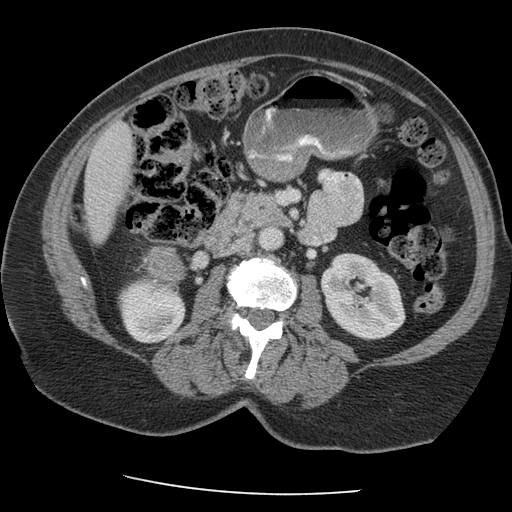
Contrast-enhanced abdominal CT, one axial slice; position 103 of 163 along the scan axis; reconstruction kernel STANDARD; 140 kVp; intravenous contrast given; soft-tissue window (W 400 / L 40 HU); 512 × 512 image matrix. Female patient, age 70 years. Case-level facts recorded for this patient, not image findings: diagnosis: adrenocortical carcinoma; tumour side: right adrenal; tumour size at pathology: 9.5 cm; Ki-67 index: 5 %; stage (as recorded): 2.
Outlined on this slice (semi-automatically segmented with operator editing):
- mass: bounding box [x1, y1, x2, y2] px = [145, 248, 186, 281]